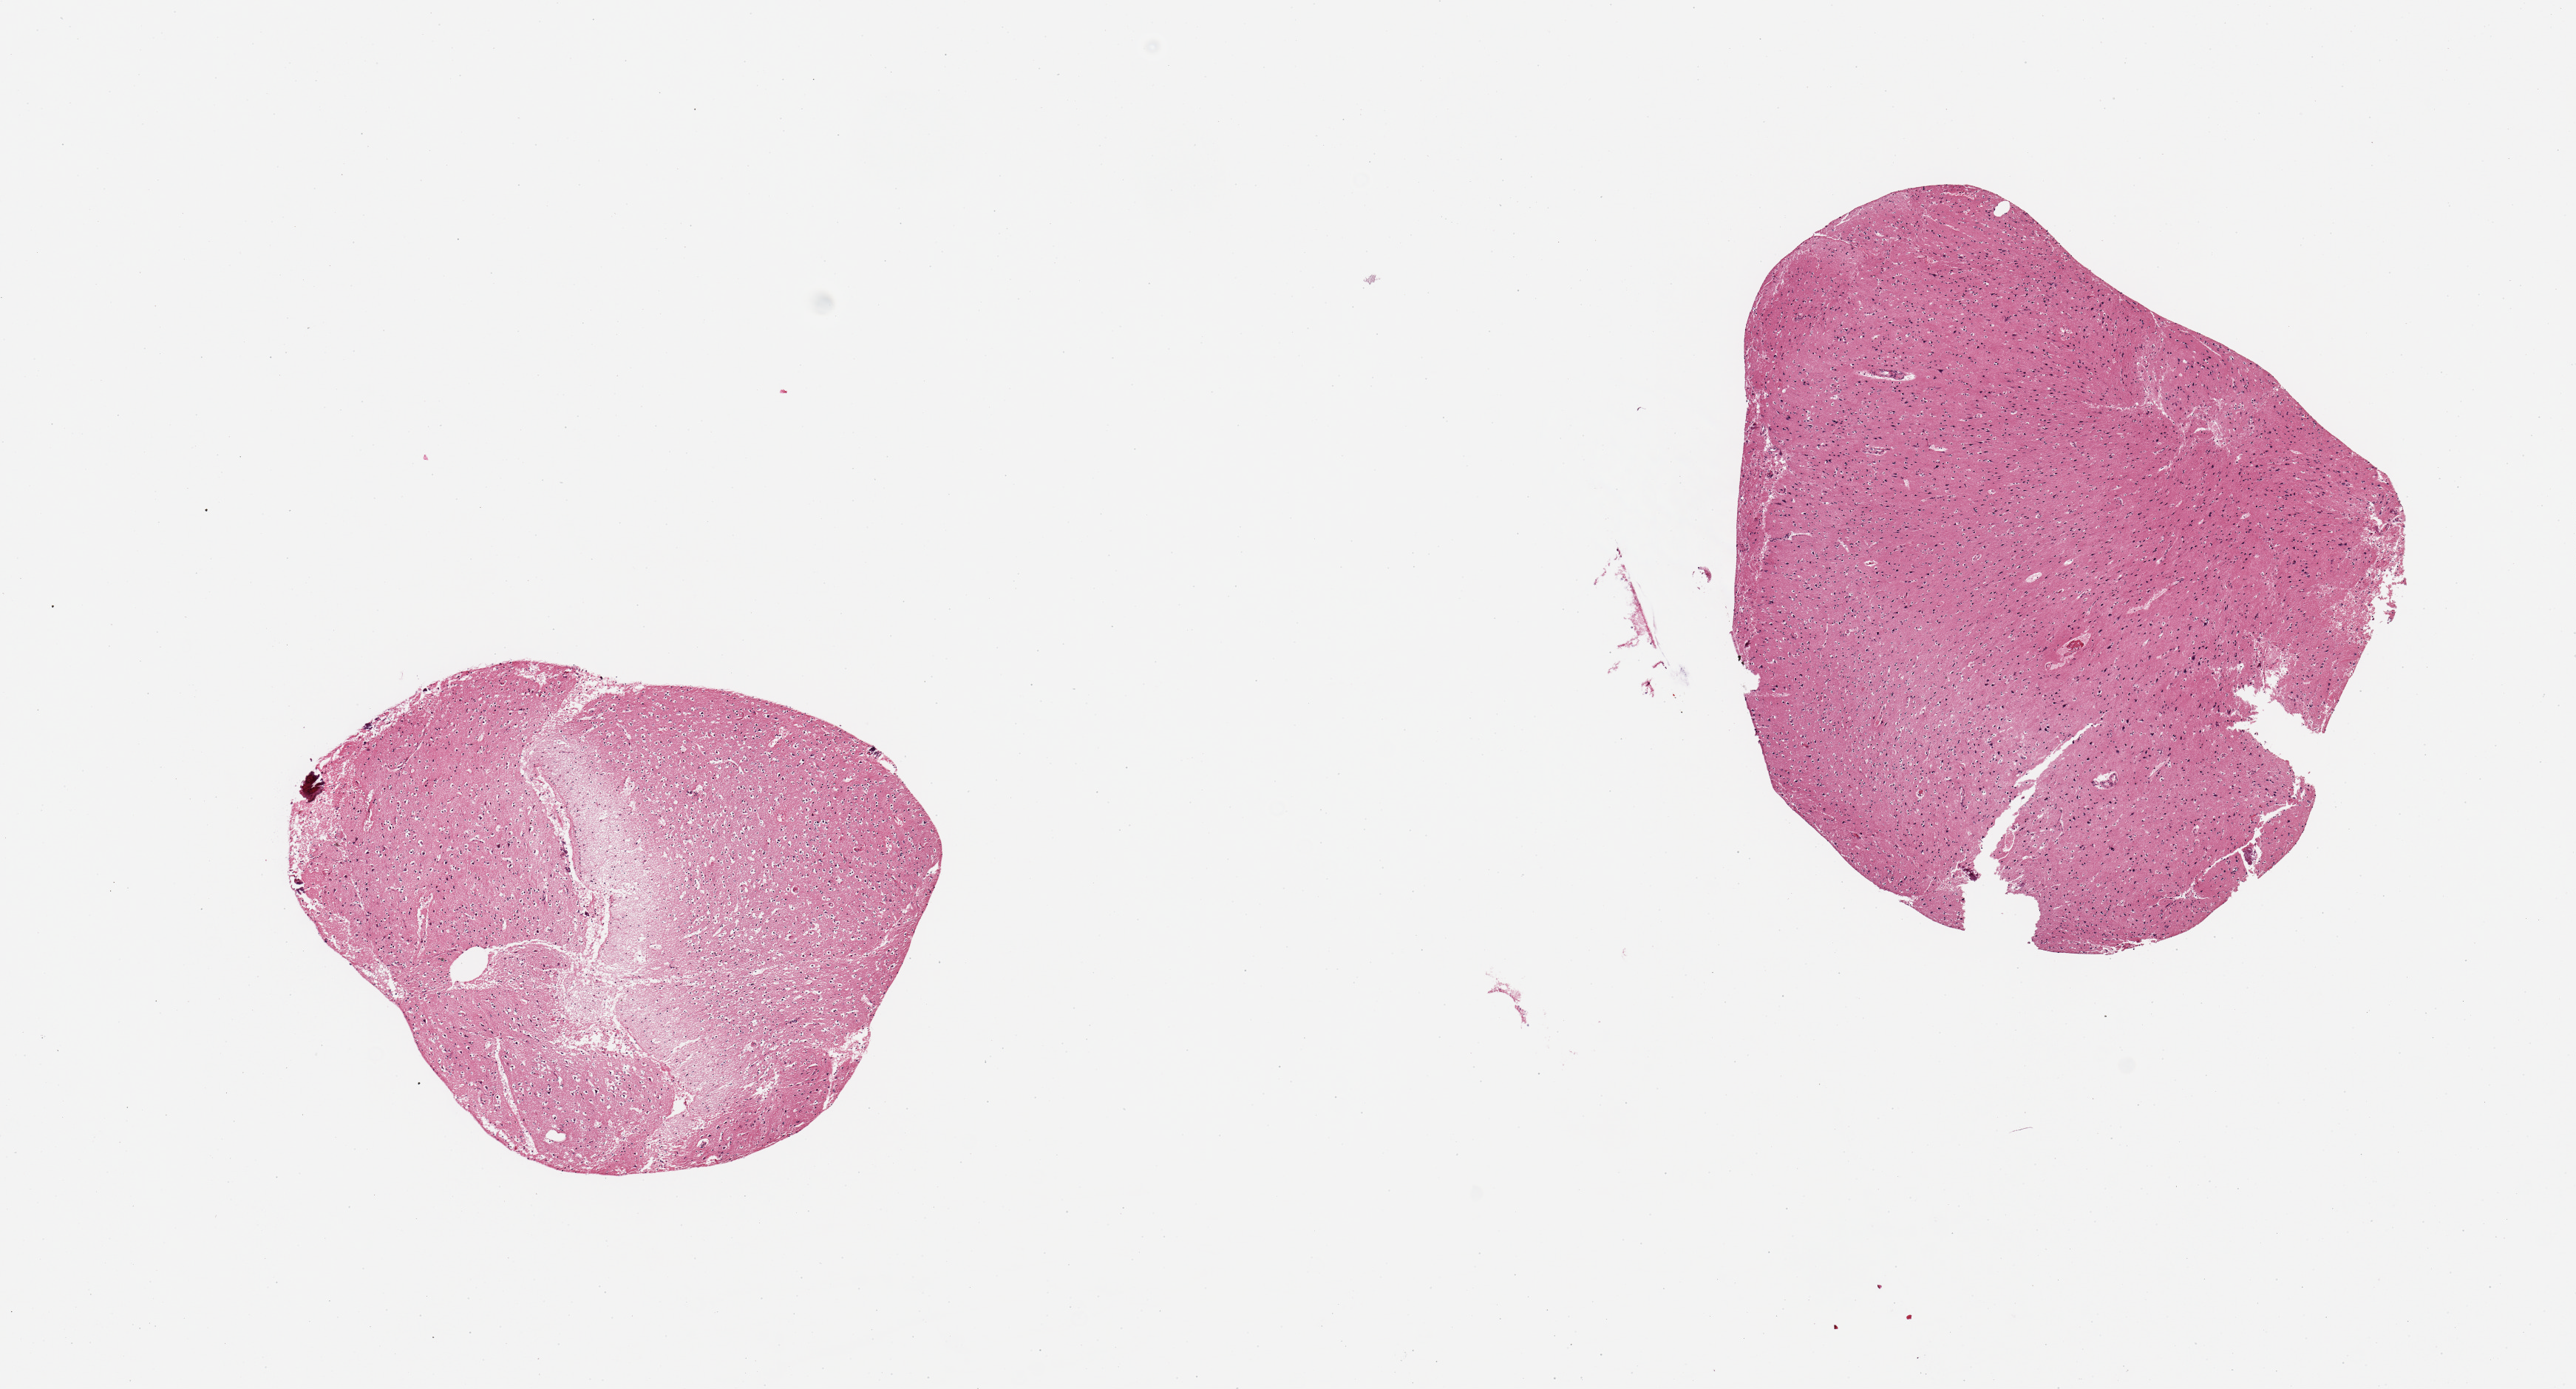
Digitized H&E-stained section, brightfield, a low-resolution overview of the entire scanned area, about 13.8 x 7.4 mm (acquisition: 20x scan), PAXgene-fixed, paraffin-embedded tissue, sampled site (target tissue): cerebral cortex, tissue donor sample. Male donor.
Review note (as recorded): 2 pieces.